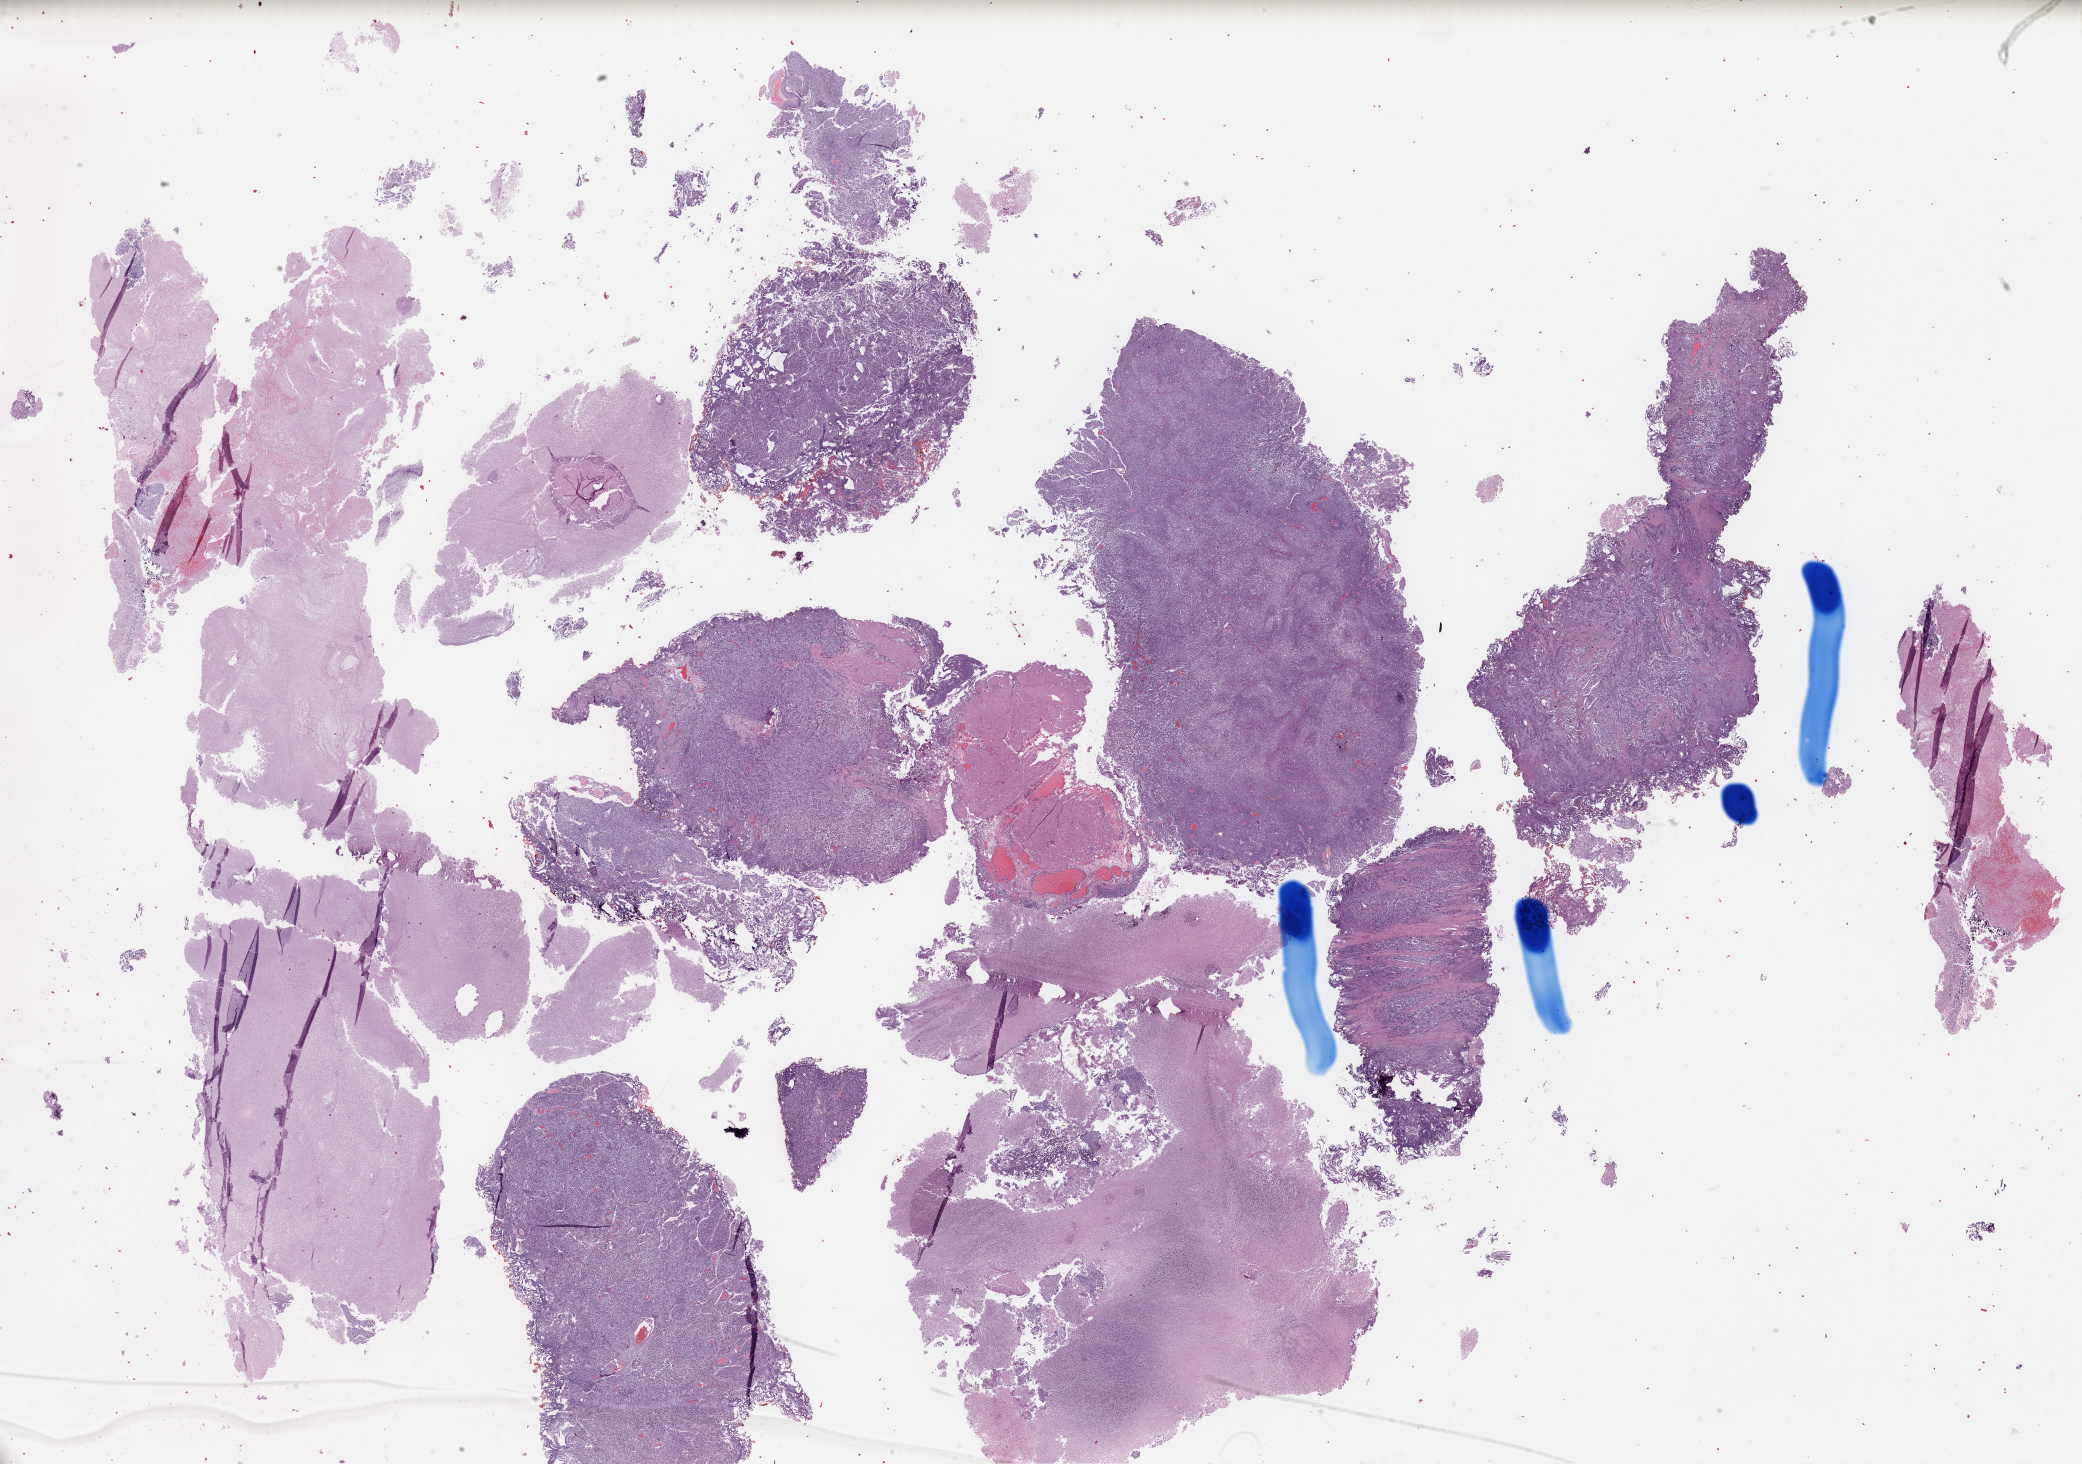
Whole-slide histology image, H&E-stained — low-resolution overview of the scanned area, about 32.7 x 23.0 mm (acquisition: 40x scan), formalin-fixed paraffin-embedded (FFPE) diagnostic section, primary tumour sample from the bladder. Male, age 65 years at initial diagnosis. Histologic grade: high grade.
AJCC pathologic stage: IV (7th edition). Pathologic diagnosis: Transitional cell carcinoma.